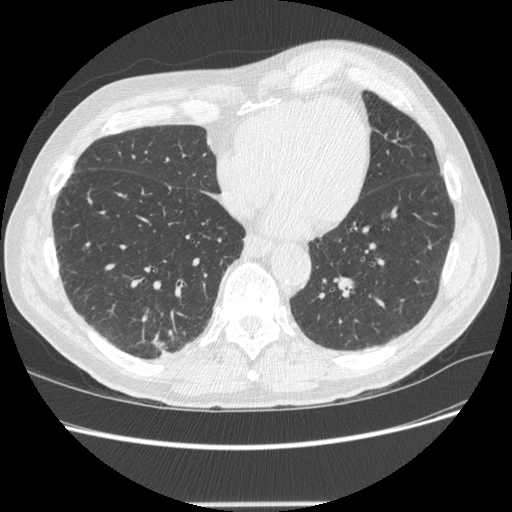
Low-dose screening chest CT, one axial slice. Position 78 of 245 along the scan axis. Reconstruction kernel STANDARD. Lung window (W 1500 / L -600 HU). 1.25 mm slice thickness. 512 × 512 image matrix.
Outlined on this slice (outlined manually by an expert reader):
- lesion 1 (tumor, lower lobe of right lung): bounding box (x1, y1, x2, y2) in pixels: (154, 337, 166, 351)